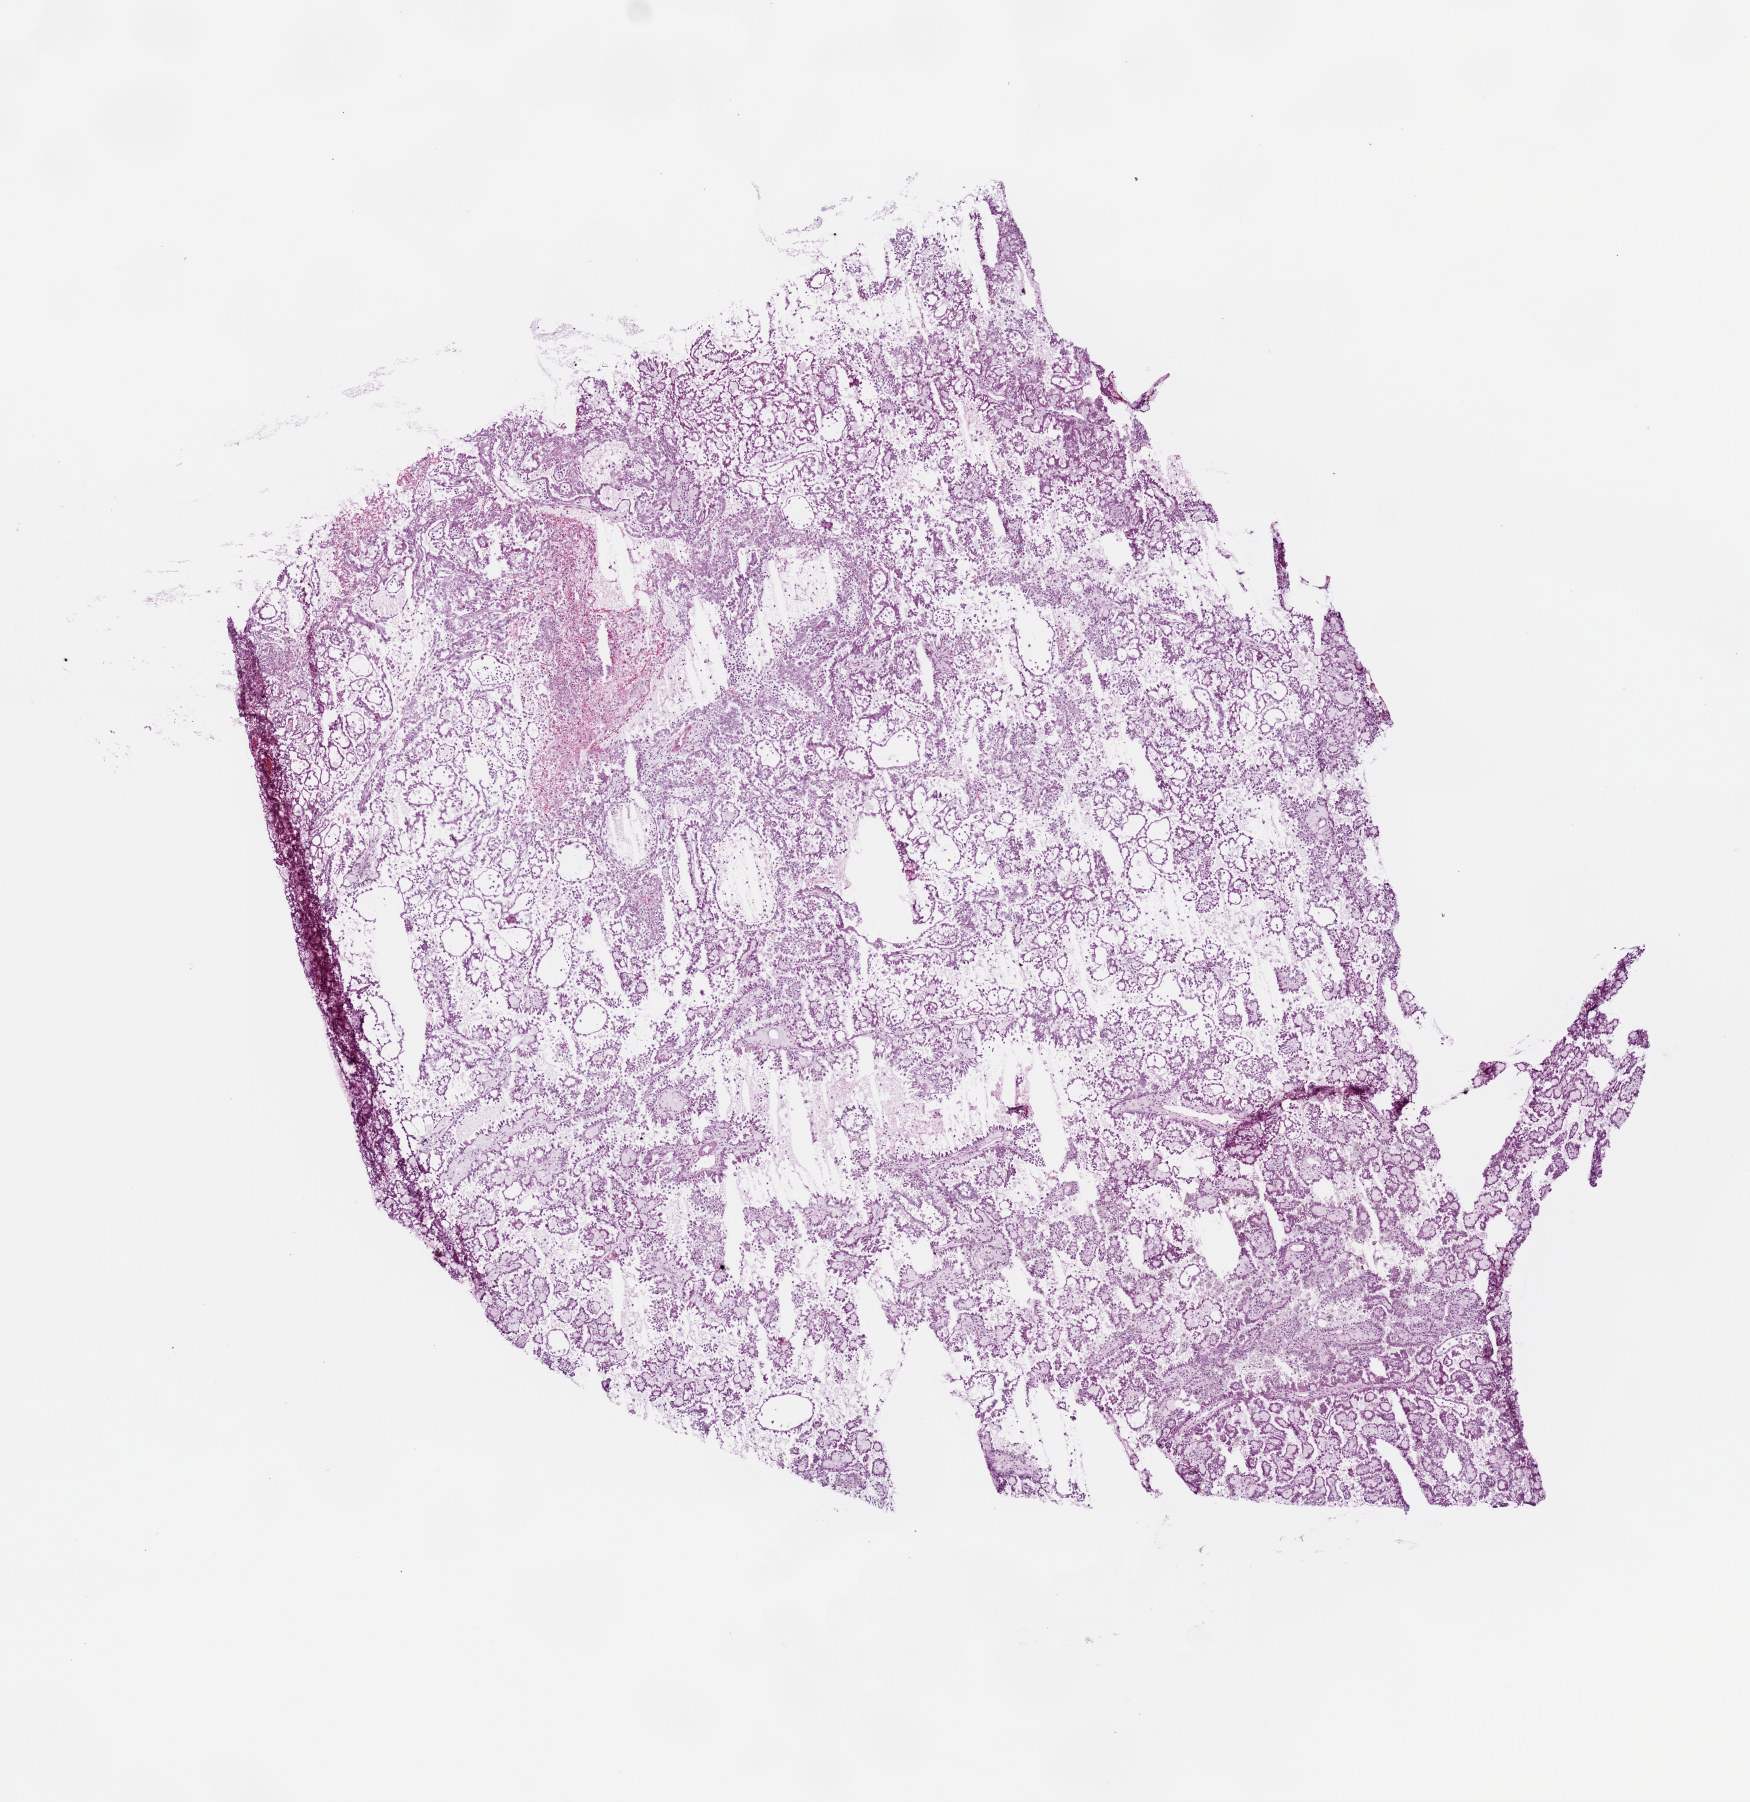
Whole-slide histology image, H&E — shown as a low-resolution overview of the whole scanned area (about 7.0 x 7.2 mm); frozen section; primary tumour sample from the kidney. Patient: male, age at initial diagnosis 51 years. Slide review estimates, as recorded: tumour cells 90%, tumour nuclei 85%, normal cells 0%, stromal cells 10%, necrosis 0%.
Laterality: left. Pathologic diagnosis: Papillary adenocarcinoma, NOS.